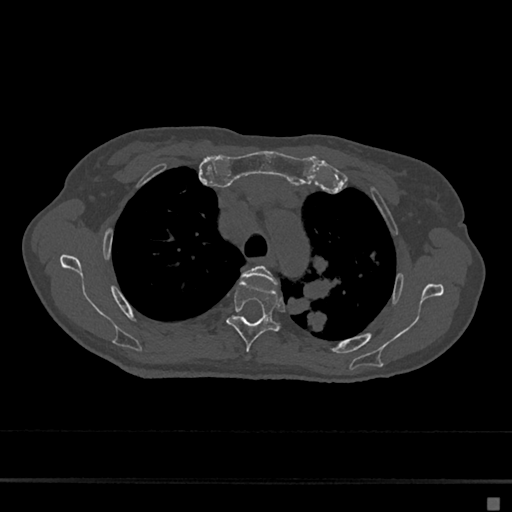
CT including the spine, one axial slice; slice 503 of 797 in the series (ordered by position); 120 kVp; bone window (W 1800 / L 400 HU); 512 × 512 image matrix, field of view 360 × 360 mm. Female patient, age 68 years. Case-level facts recorded for this patient, not image findings: primary cancer: renal.
Annotated regions visible in this slice (semi-automatic segmentation, software-assisted and operator-edited):
- T3 vertebra: bounding box [x1, y1, x2, y2] px = [242, 265, 277, 284]
- T4 vertebra: [226, 280, 279, 352]